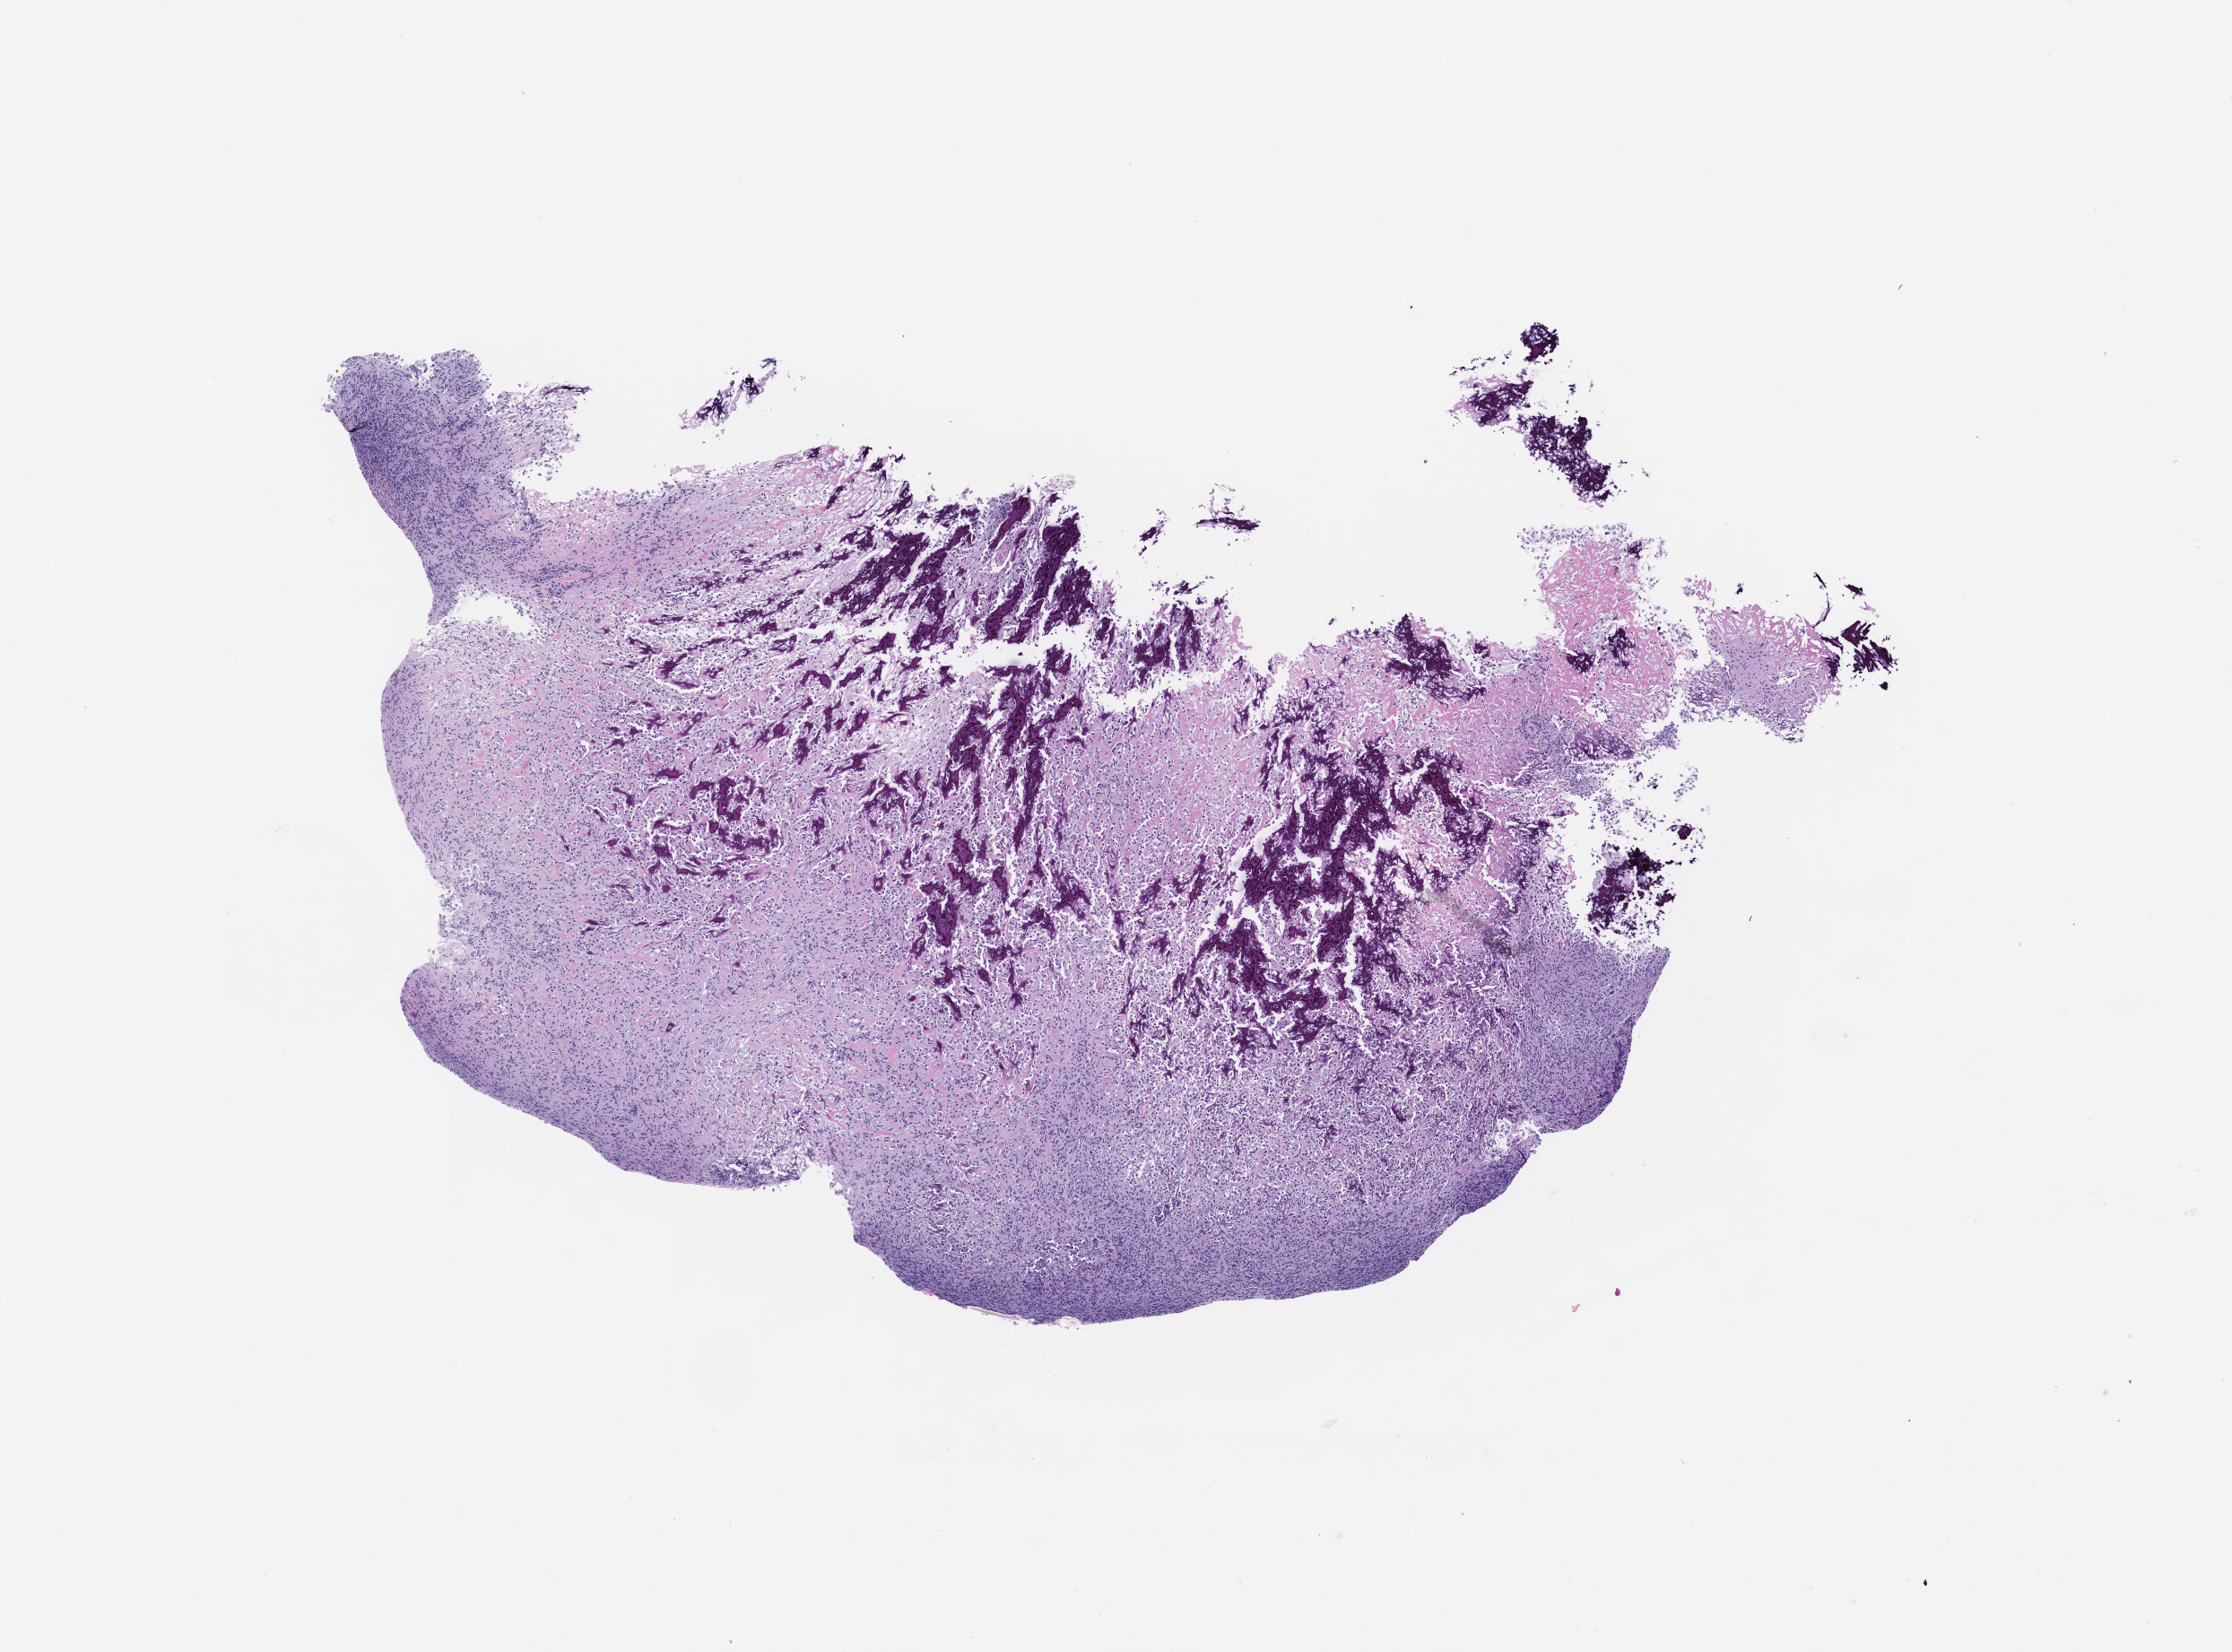
Hematoxylin and eosin (H&E) whole-slide image of a patient-derived xenograft (PDX) tumor grown in a mouse, passage 0, a low-resolution overview of the entire scanned area, about 10.0 x 7.4 mm. Formalin-fixed, paraffin-embedded (FFPE) tissue. Originating tumor site category: bone.
• originating patient diagnosis: Osteosarcoma